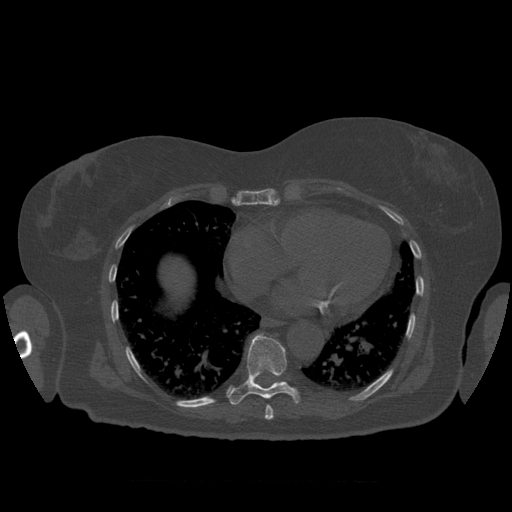
CT including the spine, one axial slice. Position 360 of 399 along the scan axis. Reconstruction kernel STANDARD. 120 kVp. Bone window (W 1800 / L 400 HU). 512 × 512 image matrix. Patient age 81 years. From the clinical record (not read from this slice): primary cancer: renal.
Outlined on this slice (semi-automatically segmented with operator editing):
- T8 vertebra: bounding box <265,405,274,420> (left, top, right, bottom; pixels)
- T9 vertebra: <227,334,300,405>